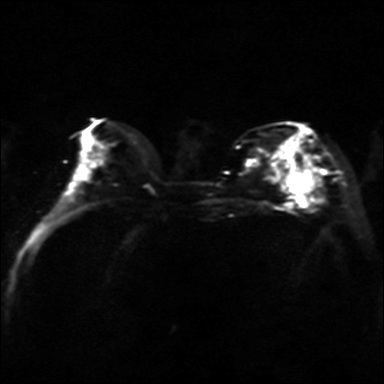
Breast MRI, one axial slice; position 17 of 36 along the scan axis; diffusion-weighted series; image 2 of 4 stored at this slice position (different b-values; order by instance number); 3 T; 384 × 384 image matrix, field of view 320 × 320 mm. Female patient.
Structures marked on this image (manually delineated by an expert):
- tumour on diffusion-weighted imaging: bounding box (x1, y1, x2, y2) in pixels: (288, 172, 311, 193)